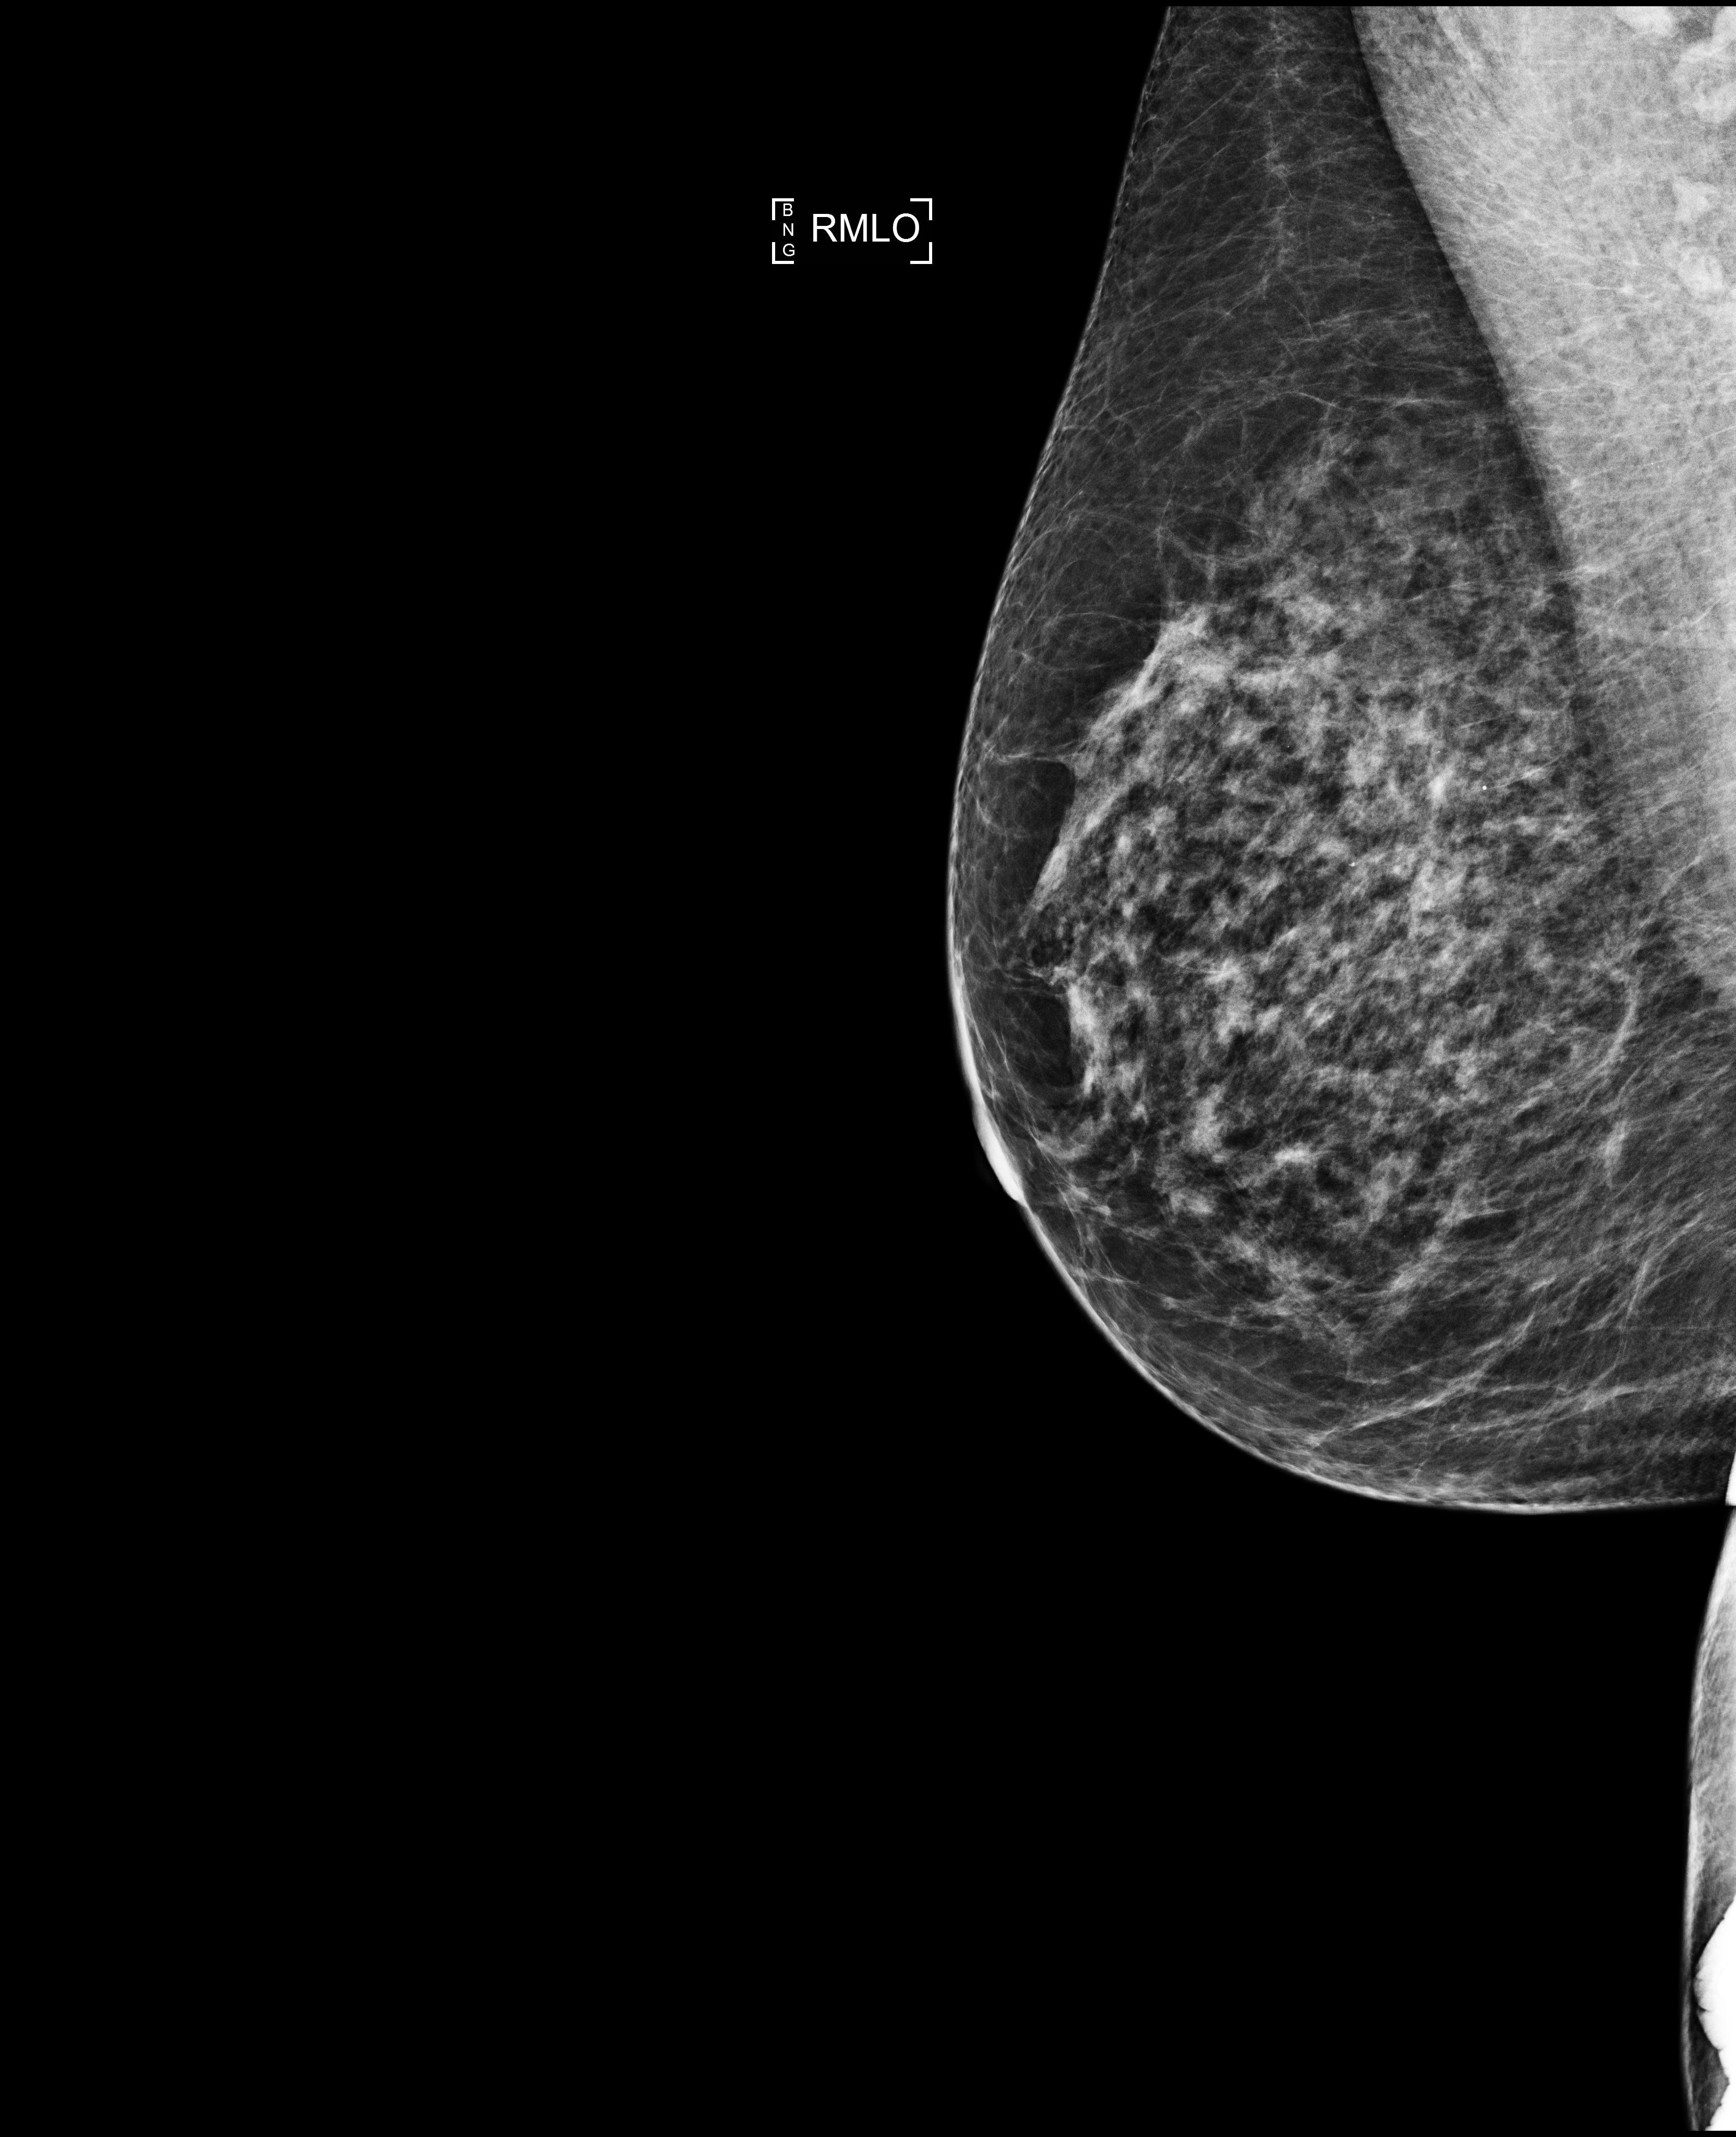
Annual screening mammography examination, compressed breast thickness 58 mm. Patient: female, 62 years.
Image type: full-field digital mammogram. Breast: right. Projection: mediolateral oblique (MLO) view.